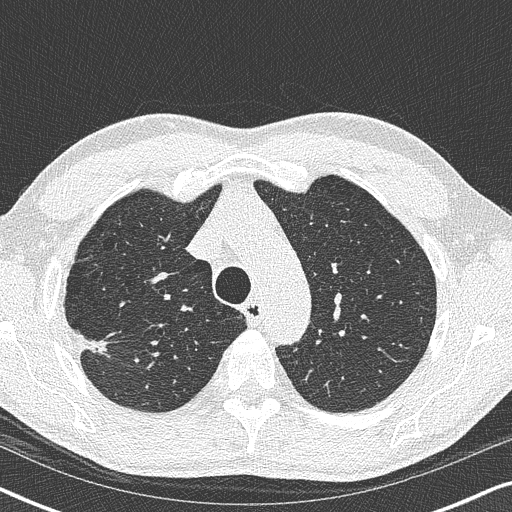
Low-dose screening chest CT, one axial slice. Position 280 of 356 along the scan axis. Reconstruction kernel B50f. 120 kVp. Lung window (W 1500 / L -600 HU). 1 mm slice thickness. 512 × 512 image matrix, field of view 330 × 330 mm.
Annotated regions visible in this slice (expert manual segmentation):
- lesion 1 (tumor, upper lobe of right lung): bounding box <80,333,106,352> (left, top, right, bottom; pixels)